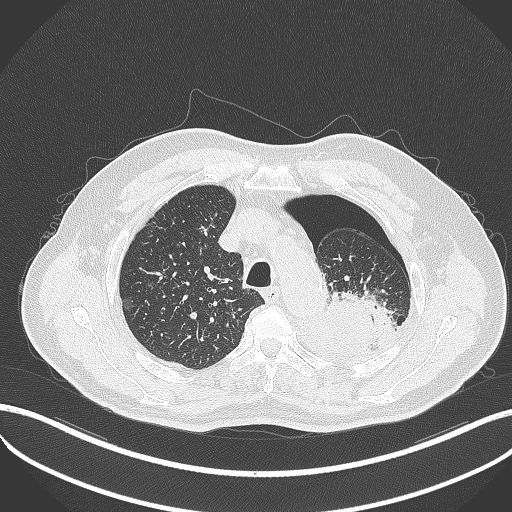
Chest CT, one axial slice. Position 396 of 464 along the scan axis. 120 kVp. Lung window (W 1500 / L -600 HU). 1 mm slice thickness. 512 × 512 image matrix. Male patient, age 76 years. Case-level facts recorded for this patient, not image findings: clinical TNM (as recorded): T3 N0 M1b.
Annotated regions visible in this slice (rectangle marked by the reading radiologist):
- lung tumour (recorded histology: adenocarcinoma): bounding box (x1, y1, x2, y2) in pixels: (304, 291, 394, 358)